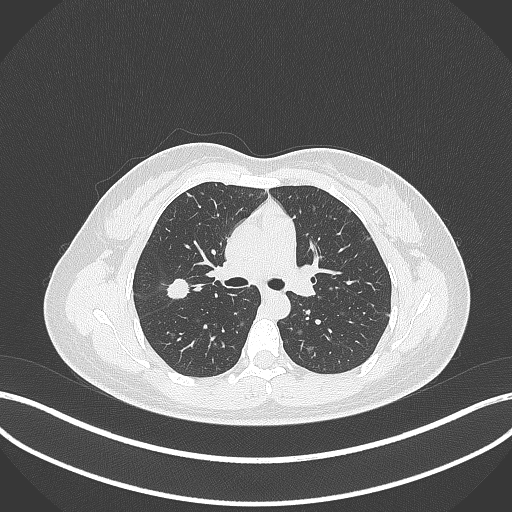
Chest CT, one axial slice; slice 209 of 307 in the series (ordered by position); 120 kVp; lung window (W 1500 / L -600 HU); 1 mm slice thickness; 512 × 512 image matrix, field of view 400 × 400 mm. Female patient, age 33 years. From the clinical record (not read from this slice): clinical TNM (as recorded): T1c N0 M0; histopathological grade: G2-G3.
Annotated regions visible in this slice (bounding box drawn by a radiologist):
- lung tumour (recorded histology: adenocarcinoma): bounding box [x1, y1, x2, y2] px = [163, 274, 191, 301]